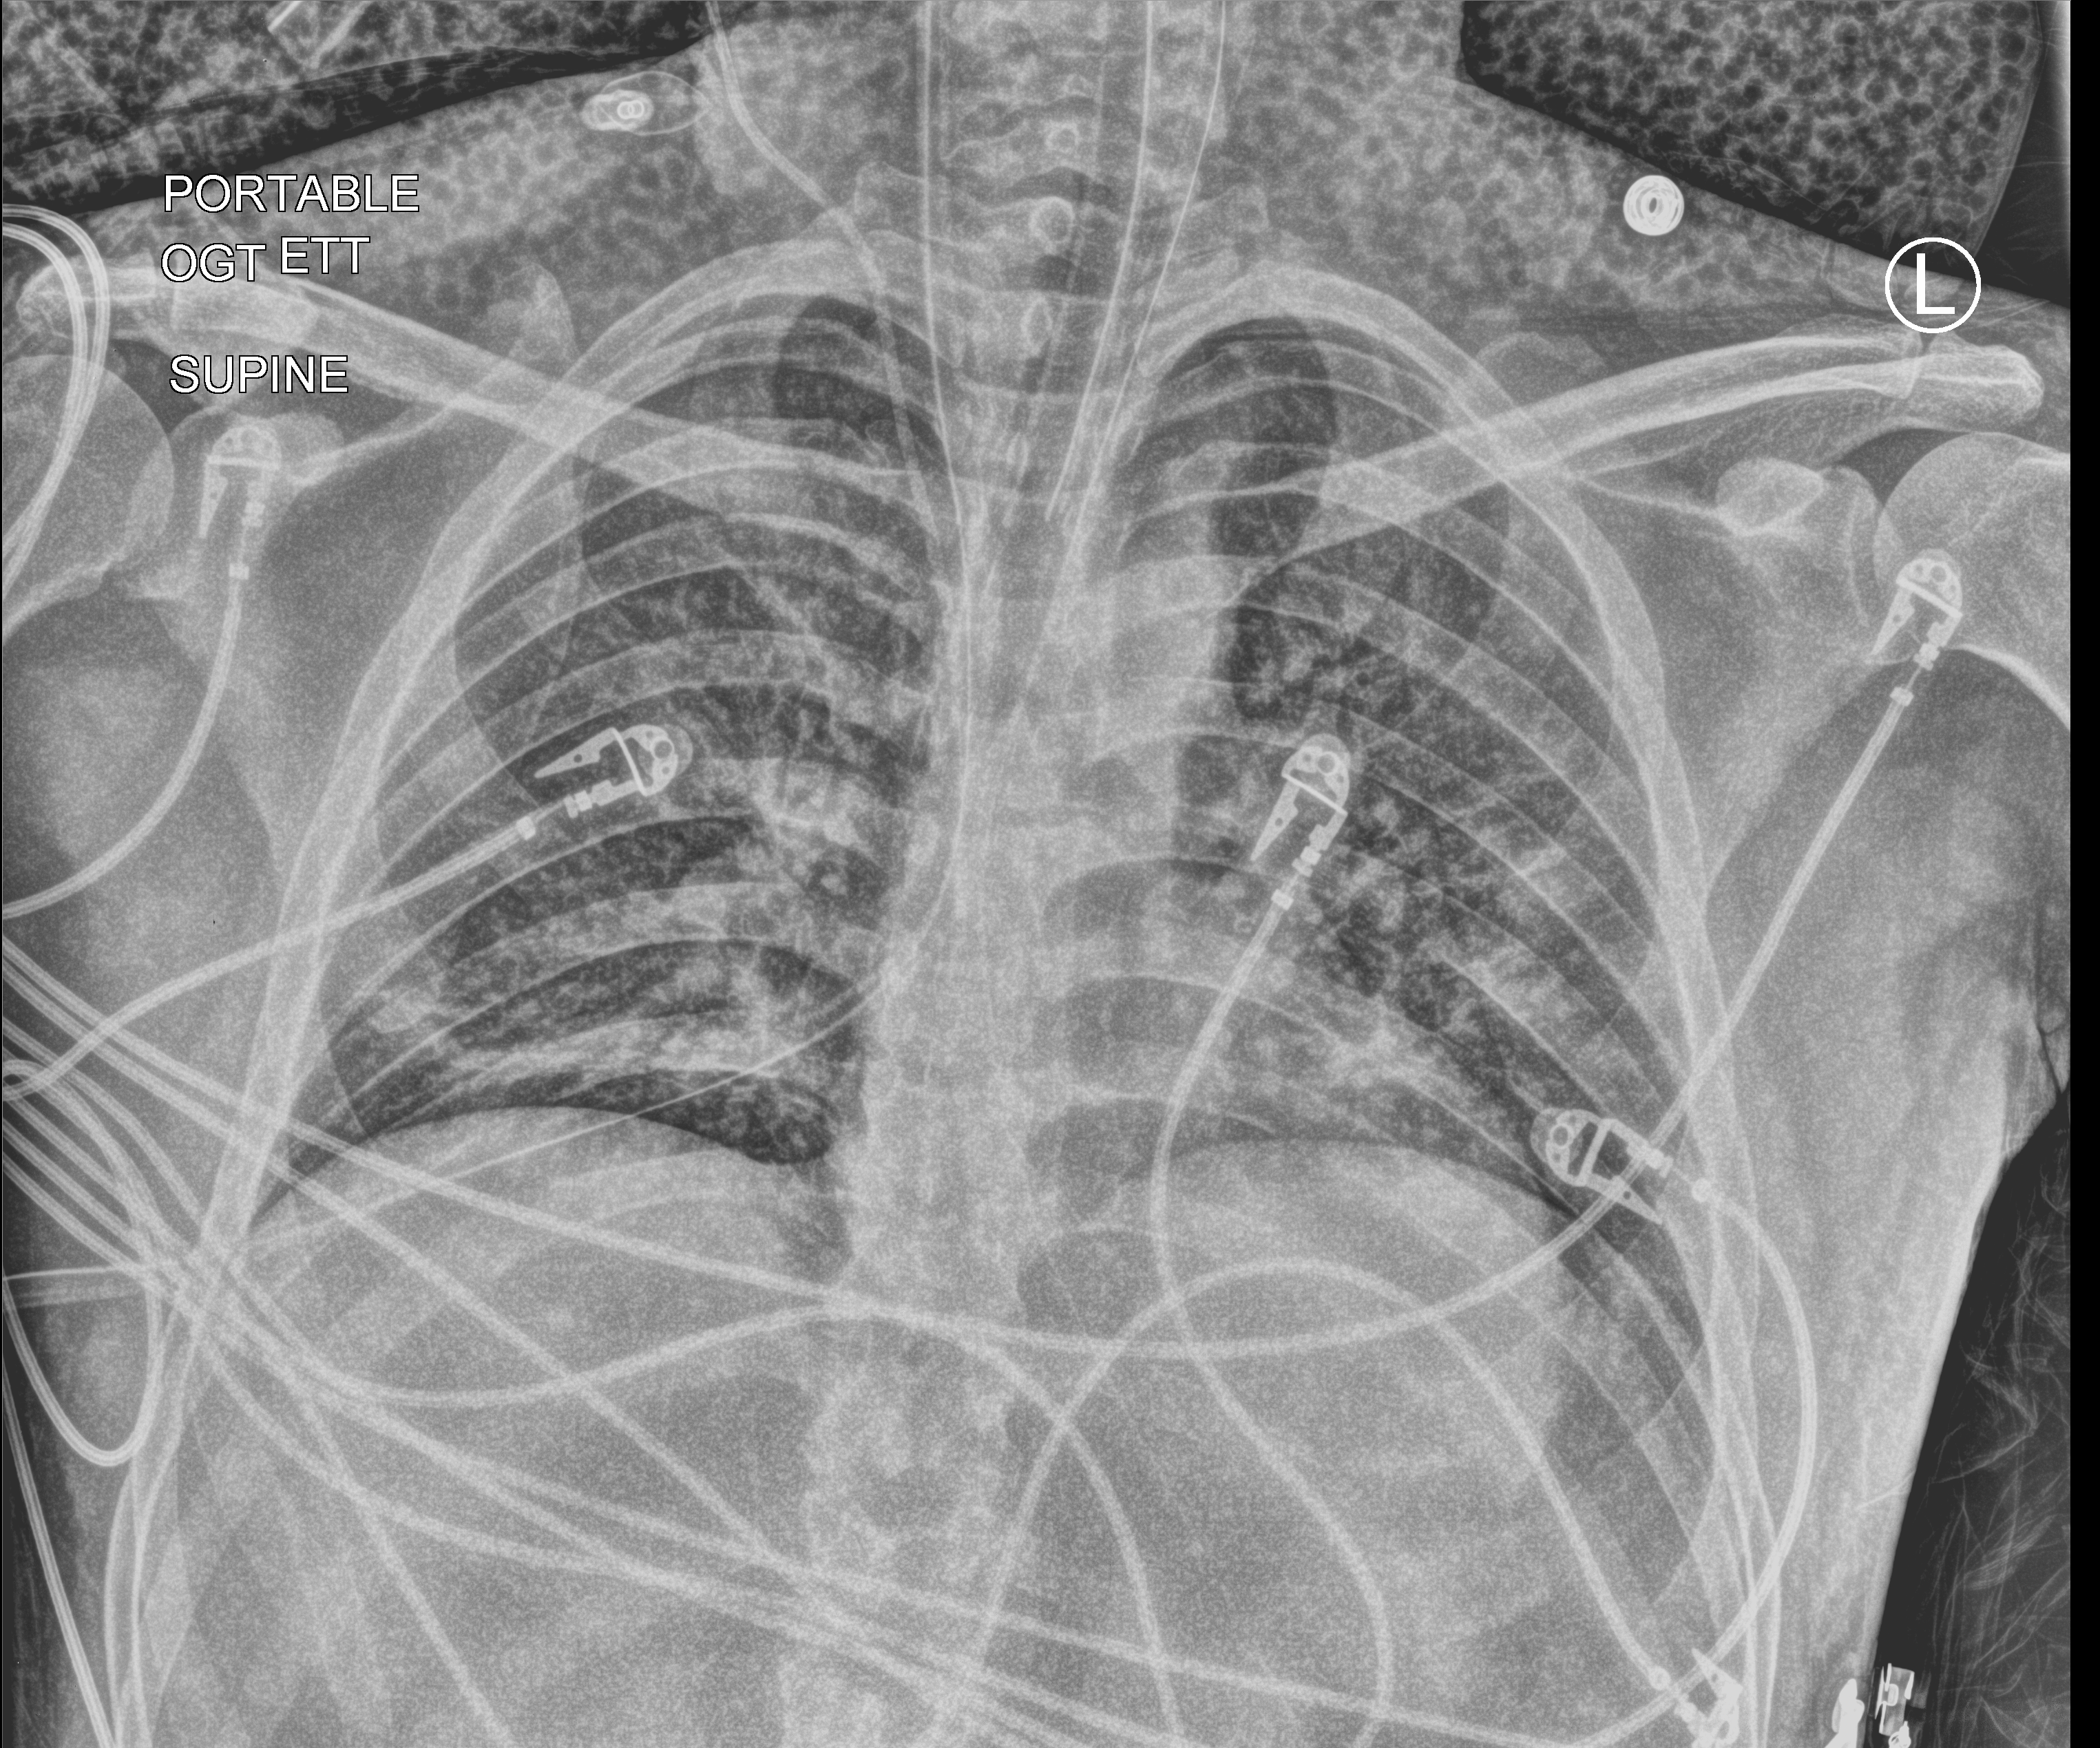
Chest X-ray (portable), anteroposterior (AP) projection. Patient hospitalised with COVID-19; male, aged 18–59 years.
From the hospital-stay record, not from the radiograph (when in the stay this image was taken is not recorded): mechanically ventilated during this hospital stay: yes; admitted to intensive care during this hospital stay: yes; length of hospital stay: 20 days.